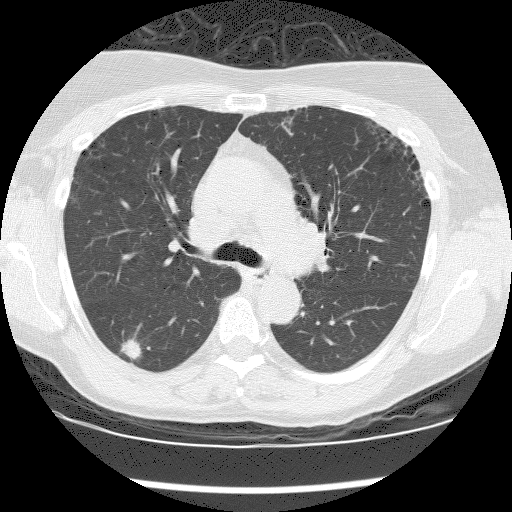
Chest CT (low-dose screening protocol), one axial image. First (baseline) screen. Lung window (W 1500 / L -600 HU). Lung (sharp) reconstruction kernel (BONE). Slice 57 of 176 in the series. Female participant, aged 59 years at enrolment.
- Expert-annotated lung lesion, bounding box <111,339,151,371> (left, top, right, bottom; pixels).
- The screening reader recorded 6 non-calcified nodules or masses ≥4 mm on this exam (right upper lobe, right upper lobe, right lower lobe, right lower lobe, right upper lobe, right upper lobe); which of them this box marks is not recorded.
- Official screen result: positive, change unspecified: nodule(s) >= 4 mm or enlarging nodule(s), mass(es), or other non-specific abnormalities suspicious for lung cancer.
- Later outcome: lung cancer diagnosed 242 days after this screen — adenocarcinoma, NOS, right lower lobe, moderately differentiated (G2), stage IIIA (AJCC 6th edition), 12 mm at pathology.